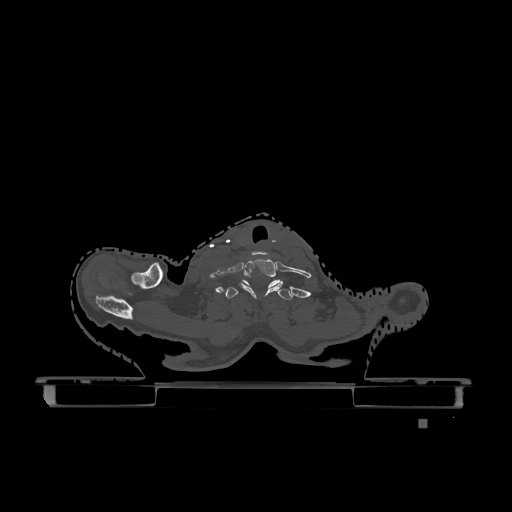
CT including the spine, one axial slice. Slice 1018 of 1317 in the series (ordered by position). Bone window (W 1800 / L 400 HU). 0.5 mm slice thickness. 512 × 512 image matrix. Patient: female, 74 years. From the clinical record (not read from this slice): primary cancer: lung; vertebrae with lytic lesions (as recorded): T1, T4, T5, T6, L4, L5.
Annotated regions visible in this slice (semi-automatic segmentation, software-assisted and operator-edited):
- T1 vertebra: bounding box (x1, y1, x2, y2) in pixels: (225, 280, 293, 300)